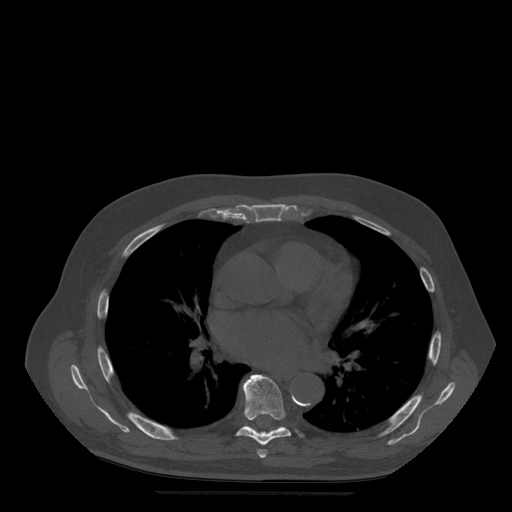
CT including the spine, one axial slice; bone window (W 1800 / L 400 HU); 1.25 mm slice thickness; 512 × 512 image matrix, field of view 420 × 420 mm. Patient age 72 years. From the clinical record (not read from this slice): primary cancer: prostate.
Structures marked on this image (semi-automatic segmentation, software-assisted and operator-edited):
- T6 vertebra: bounding box [x1, y1, x2, y2] px = [257, 450, 268, 459]
- T7 vertebra: [236, 375, 291, 446]
- T8 vertebra: [245, 426, 284, 430]